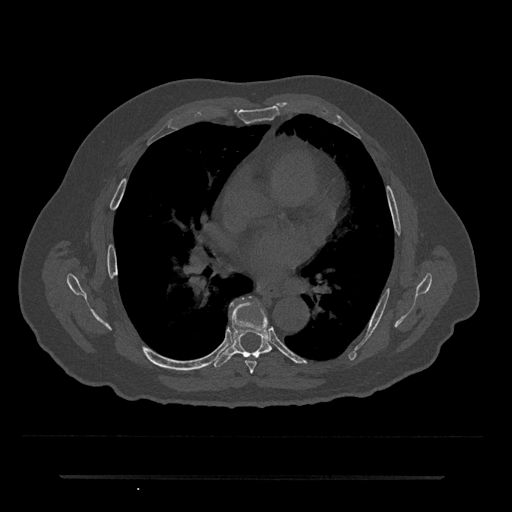
CT including the spine, one axial slice. Position 407 of 797 along the scan axis. Reconstruction kernel Br40s/3. 120 kVp. Bone window (W 1800 / L 400 HU). 0.5 mm slice thickness. 512 × 512 image matrix, field of view 437 × 437 mm. Male patient, age 69 years. Case-level facts recorded for this patient, not image findings: primary cancer: prostate.
Structures marked on this image (semi-automatically segmented with operator editing):
- T6 vertebra: bounding box (x1, y1, x2, y2) in pixels: (245, 361, 256, 373)
- T7 vertebra: (214, 301, 272, 368)